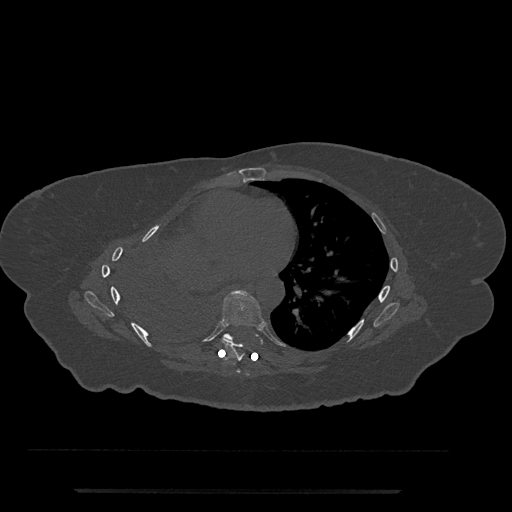
CT including the spine, one axial slice; slice 428 of 797 in the series (ordered by position); 120 kVp; bone window (W 1800 / L 400 HU); 0.5 mm slice thickness; 512 × 512 image matrix, field of view 440 × 440 mm. Female patient, age 51 years. From the clinical record (not read from this slice): primary cancer: neuro.
Outlined on this slice (semi-automatic segmentation, software-assisted and operator-edited):
- T6 vertebra: bounding box <237,369,241,373> (left, top, right, bottom; pixels)
- T7 vertebra: <221,291,263,361>
- T8 vertebra: <222,333,233,340>